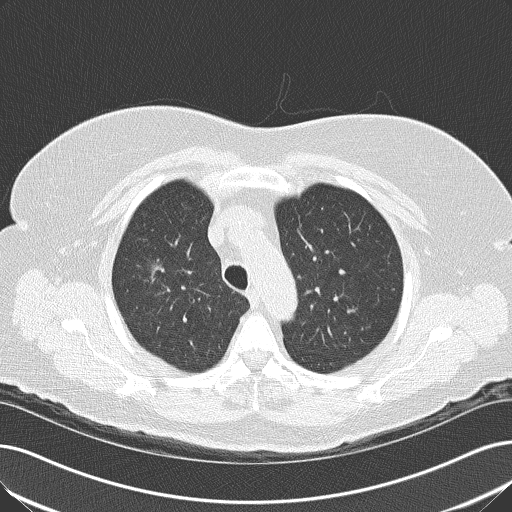
Low-dose screening chest CT, axial slice, baseline annual screen, lung window (W 1500 / L -600 HU), 512 × 512 image matrix. Female, age 74 years at enrolment.
Expert reader's lesion annotation, bounding box [x1, y1, x2, y2] px = [132, 244, 192, 300]. The screening reader recorded 2 non-calcified nodules or masses ≥4 mm on this exam; which of them this box marks is not recorded.